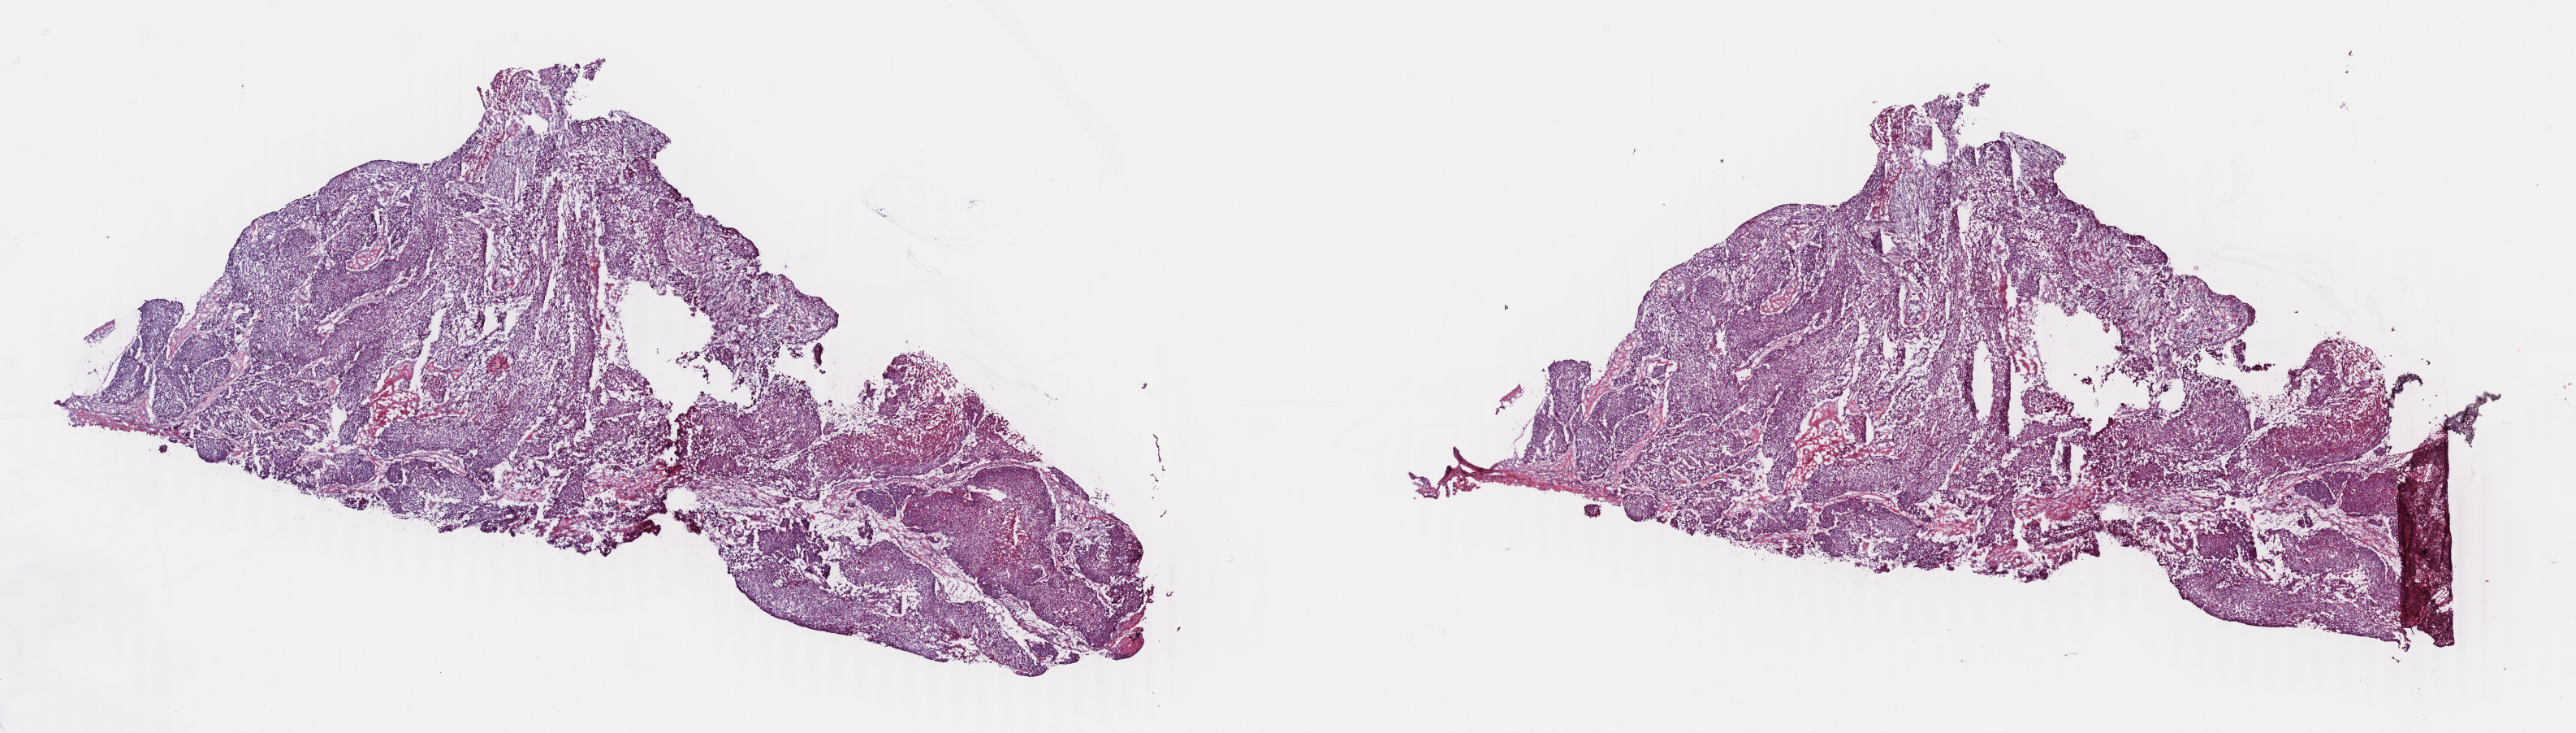
H&E whole-slide image — whole scanned area (about 25.2 x 7.2 mm, acquisition: 40x scan) shown as a low-resolution overview; frozen section from the top of the tissue portion; sample: primary tumour, bladder. Male patient; age at initial diagnosis 71 years. Histologic grade: high grade. Composition of this section per pathologist review: tumour cells 78%, tumour nuclei 85%, normal cells 0%, stromal cells 20%, necrosis 2%. Inflammatory infiltration, as recorded: lymphocyte infiltration 10%, monocyte infiltration 0%, neutrophil infiltration 0%.
- TNM: T3b N0 M0
- diagnosis: Transitional cell carcinoma
- AJCC pathologic stage: III (5th edition)